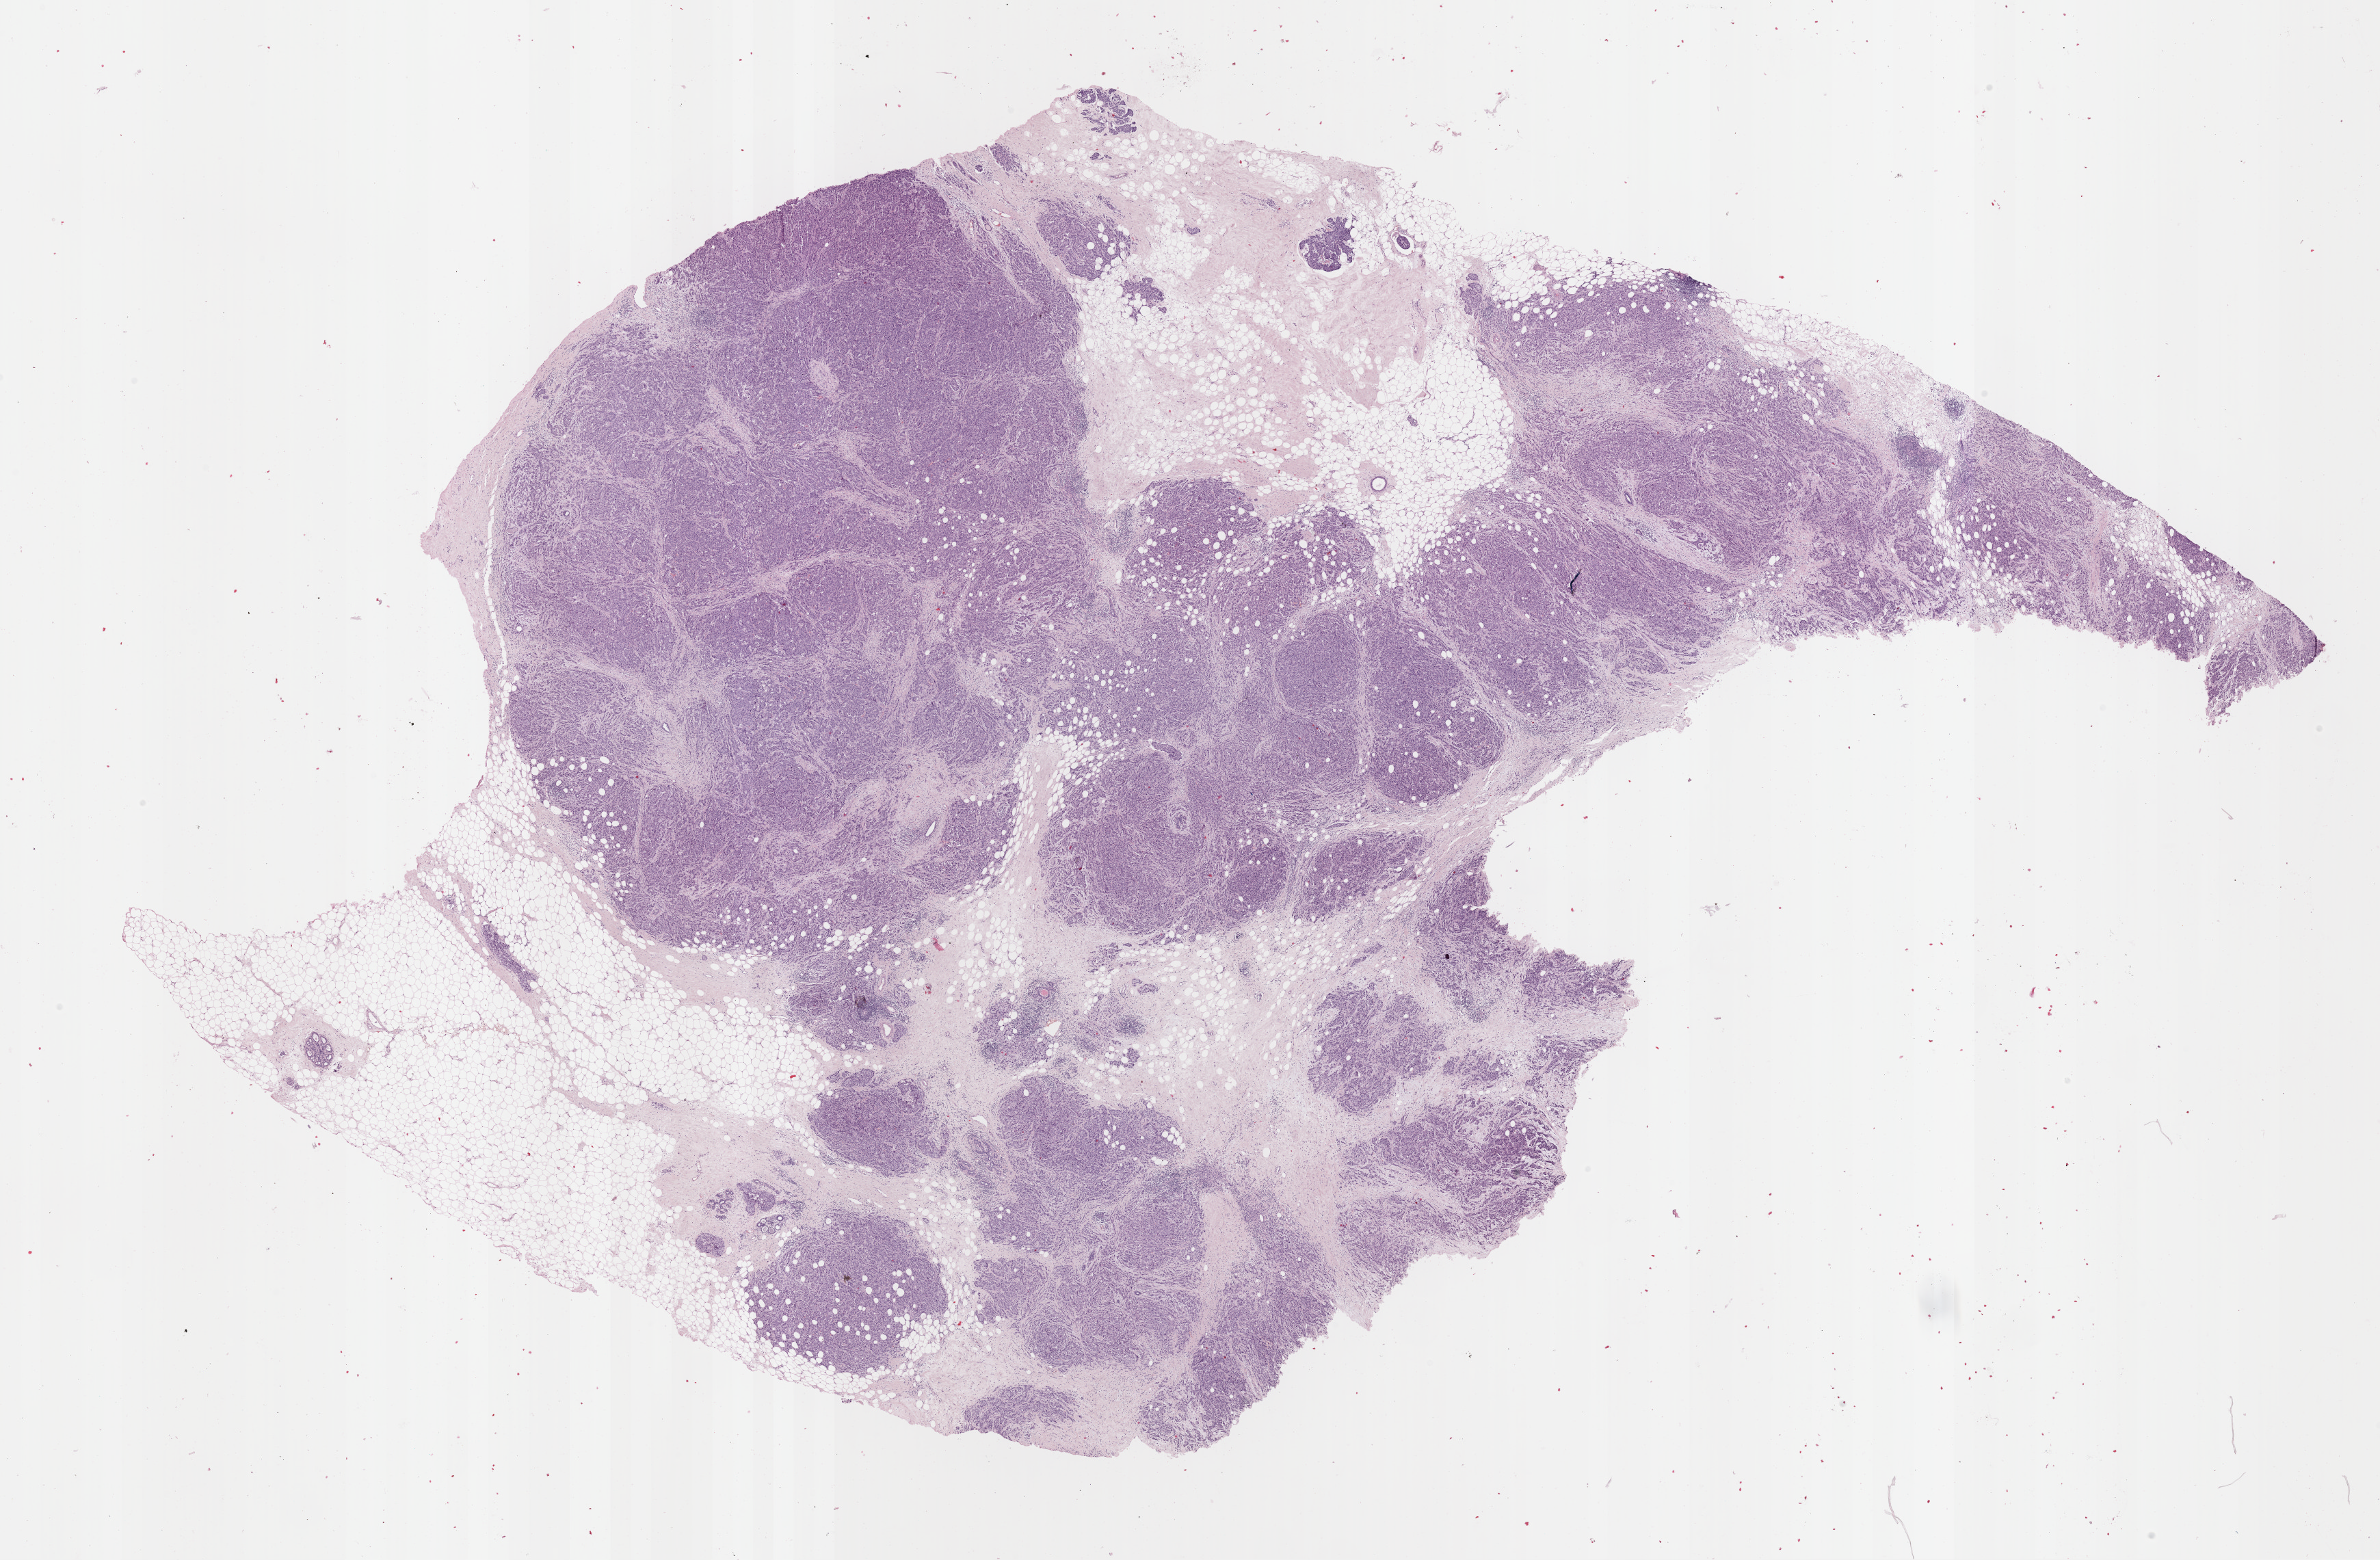
H&E whole-slide image, shown as a low-resolution overview of the whole scanned area (about 27.5 x 18.0 mm), formalin-fixed paraffin-embedded (FFPE) diagnostic section, primary tumour sample from the breast. Female, age 61 years at initial diagnosis.
AJCC pathologic stage: IIIA. TNM: T2 N2a MX. Pathologic diagnosis: Infiltrating duct carcinoma, NOS.